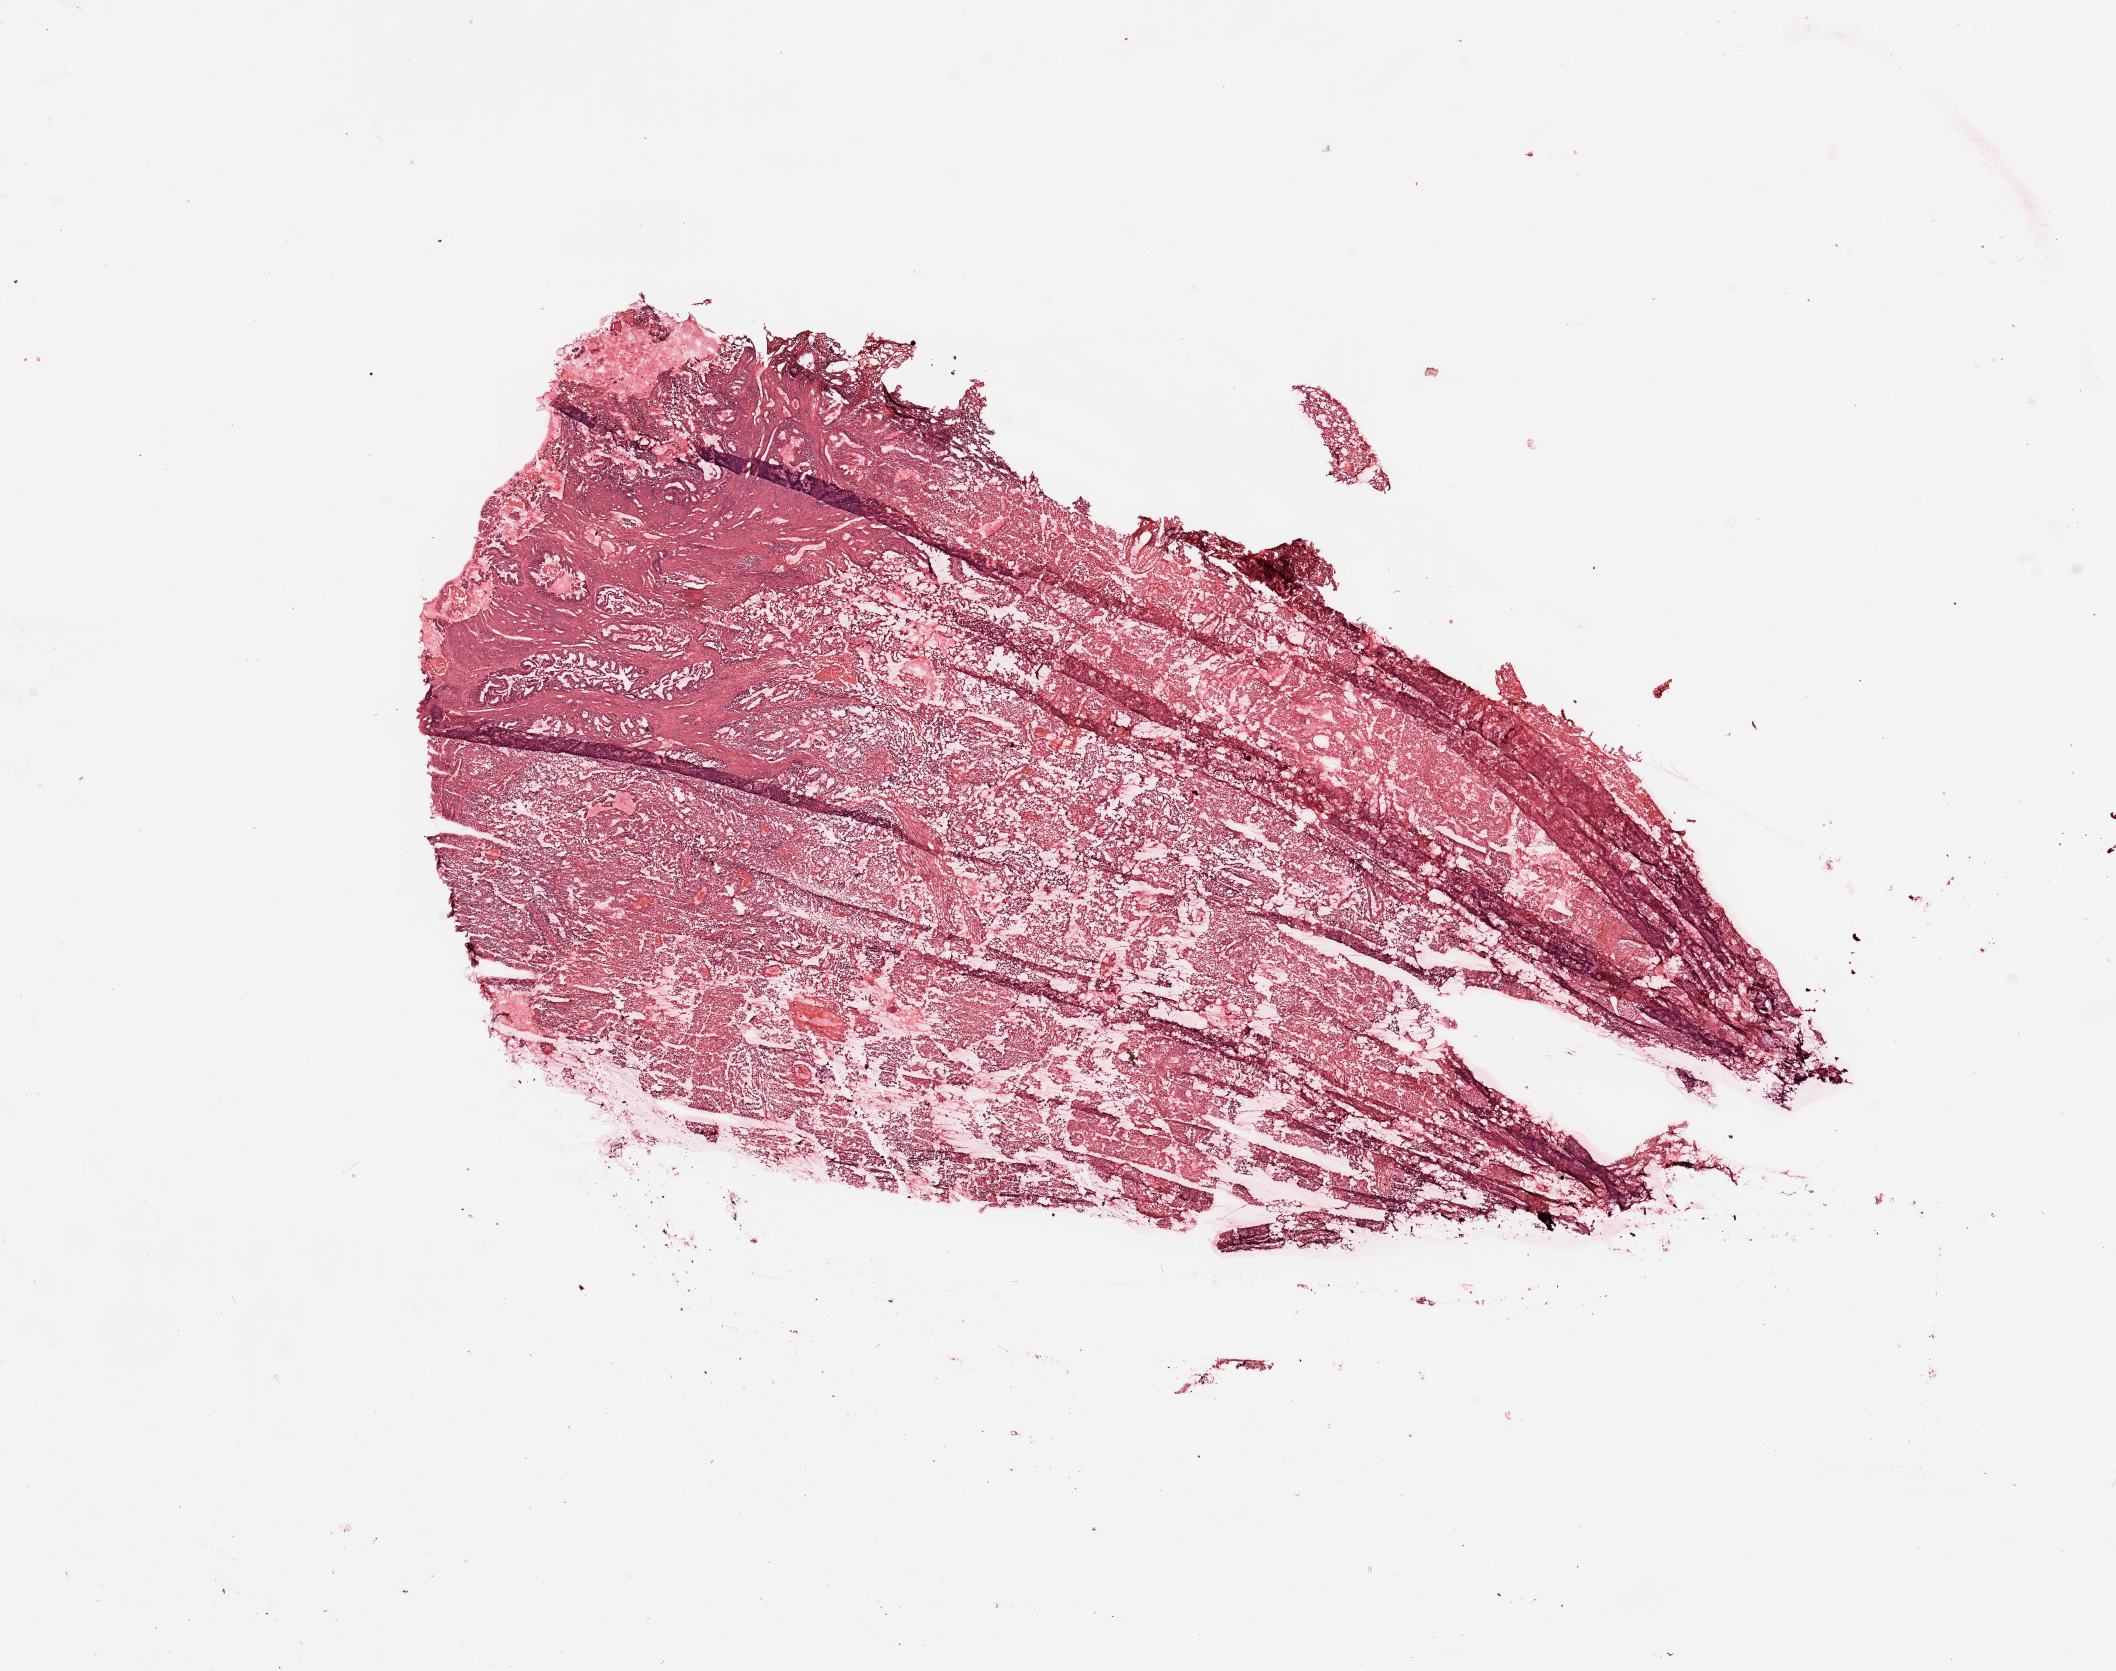
H&E-stained whole-slide image, whole scanned area (about 16.7 x 13.2 mm, acquisition: 20x scan) shown as a low-resolution overview, uterus, tumour tissue. 67-year-old female patient. Histologic grade: G2 (moderately differentiated).
Diagnosis: Endometrioid adenocarcinoma, NOS. AJCC pathologic stage: I.